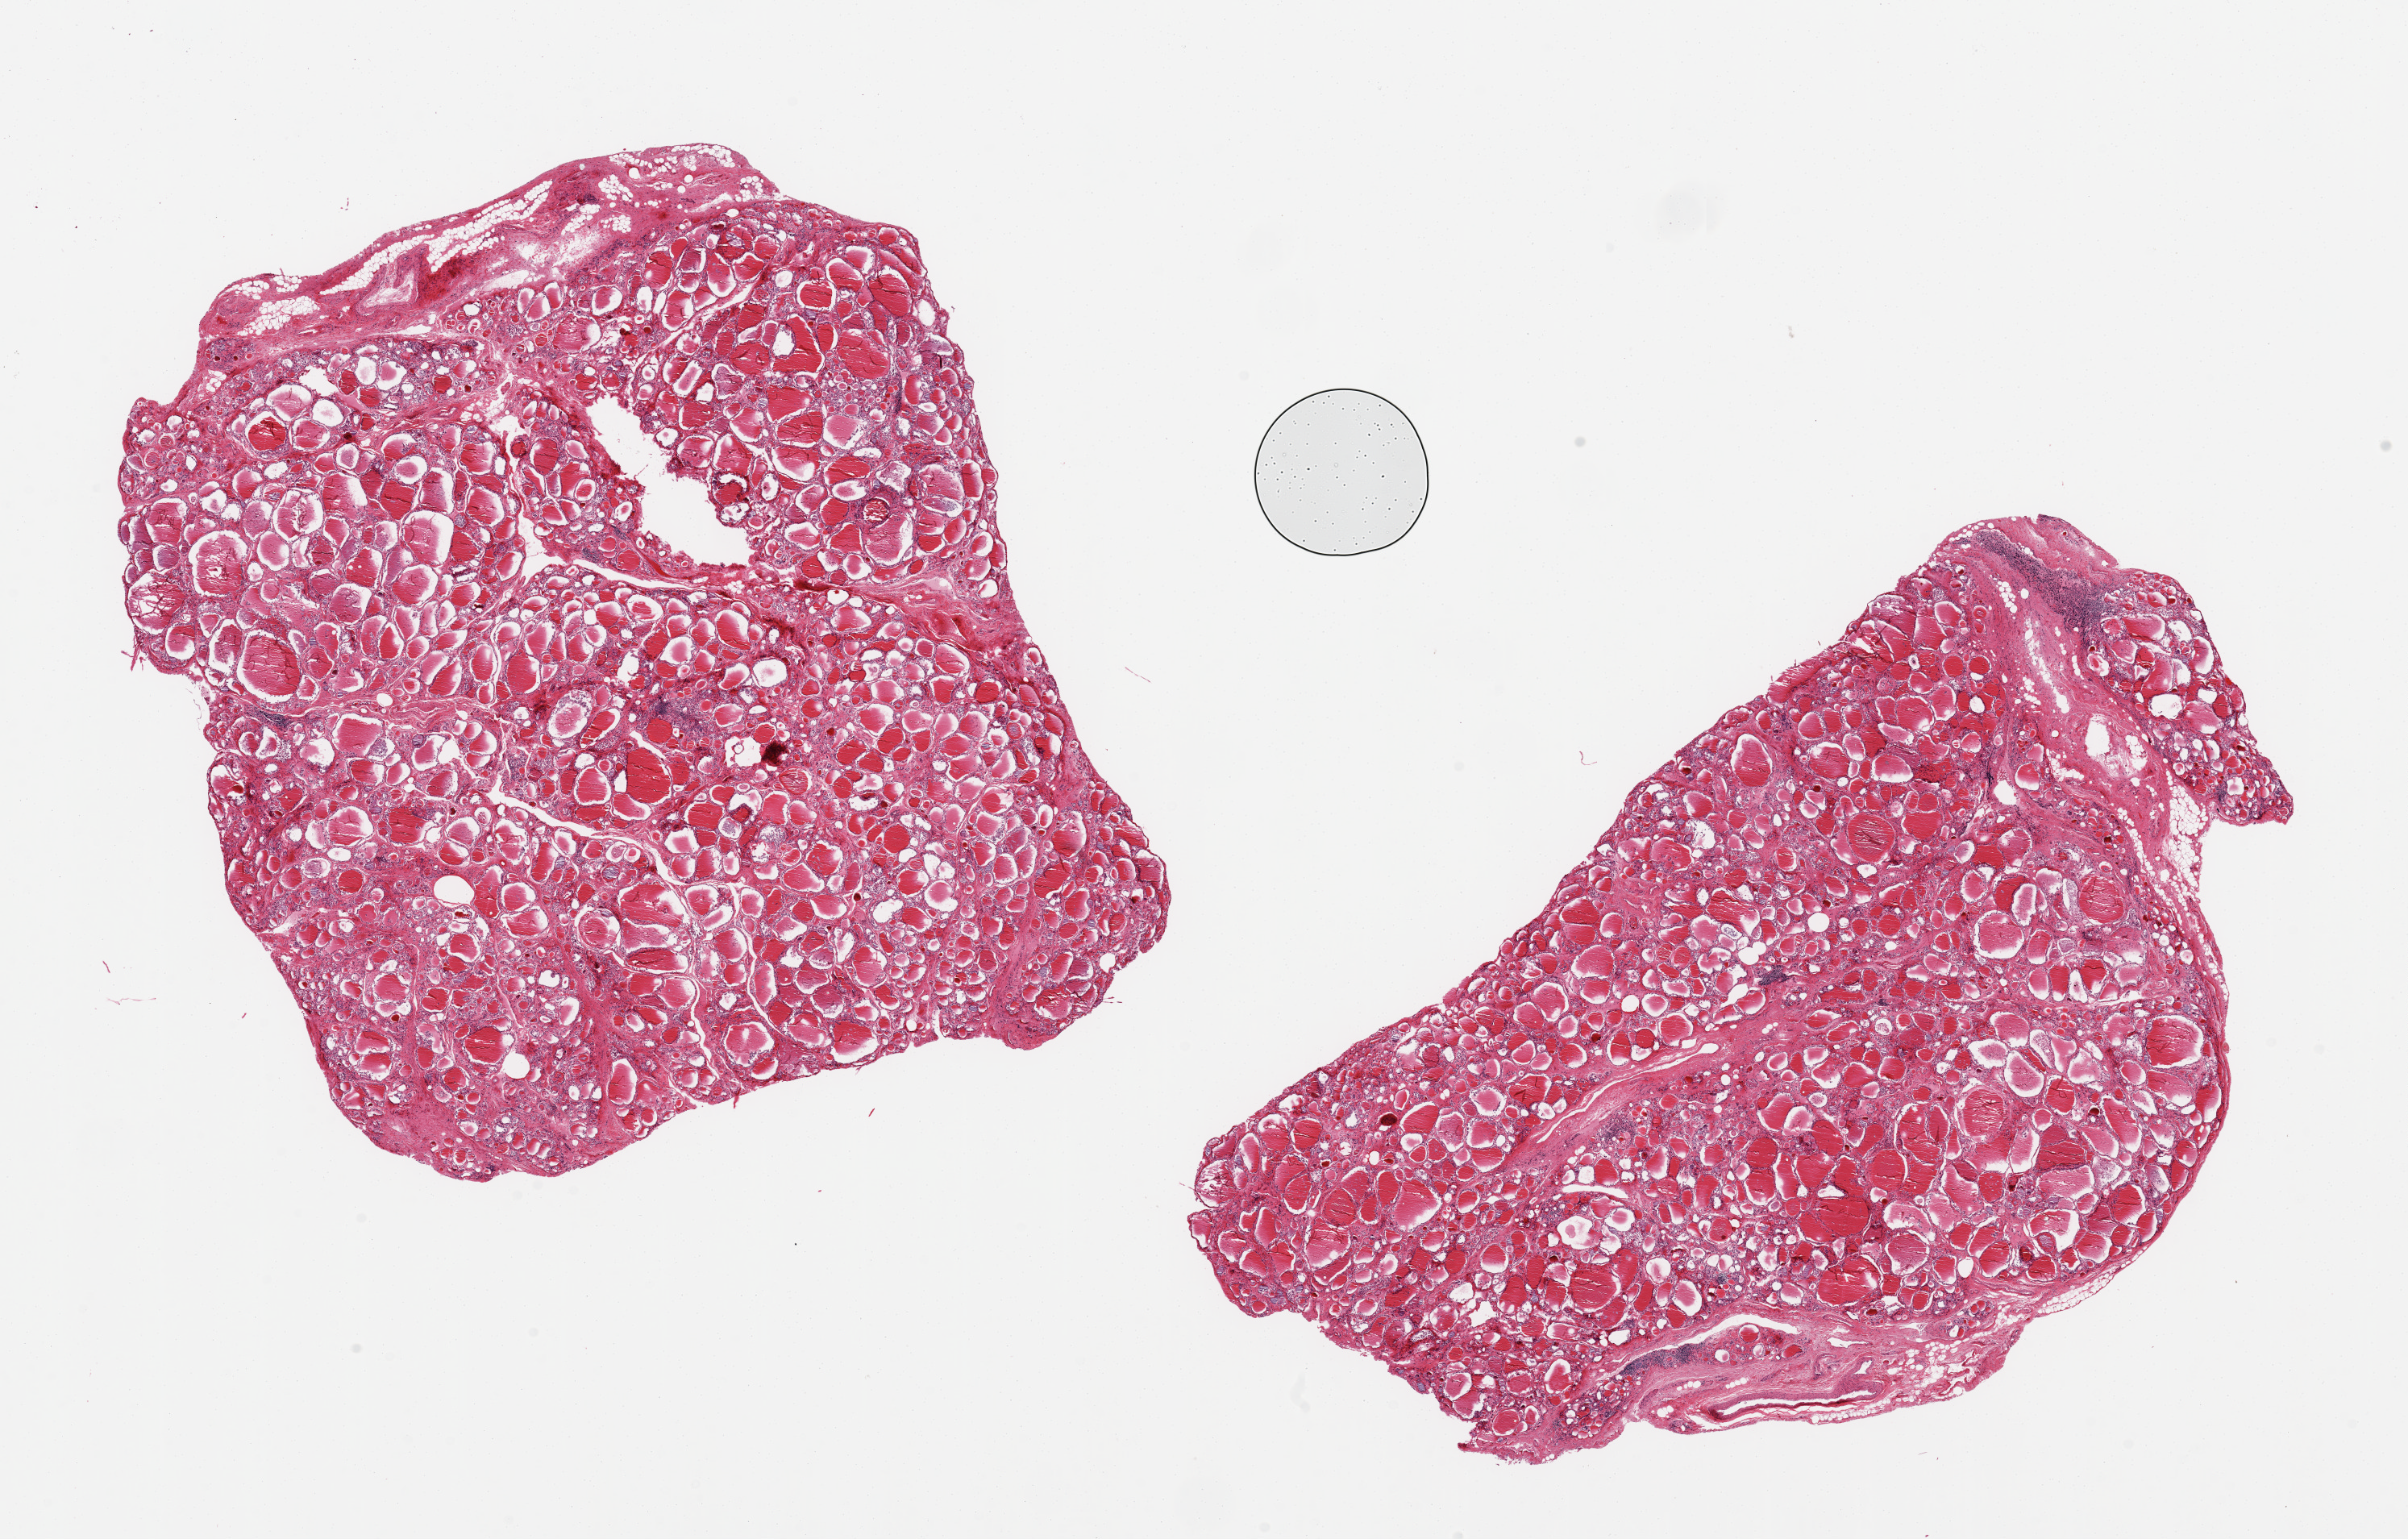
Whole-slide image, haematoxylin and eosin stain — whole scanned area (about 23.6 x 15.1 mm) shown as a low-resolution overview; PAXgene-fixed paraffin-embedded (PFPE) section; sampled site (target tissue): thyroid; donor tissue sample. Donor: male.
- pathologist's review note for this sample: 2 pieces; nodularity with scattered groups of lymphocytes